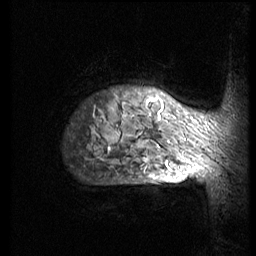
Breast MRI (dynamic contrast-enhanced), one sagittal slice. Position 66 of 74 along the scan axis. 3 images stored at this slice position (order not interpretable as contrast timing). 1.5 T. TE 4.2 ms, TR 8.9 ms. 2.5 mm slice thickness. 256 × 256 image matrix, field of view 200 × 200 mm. Female patient, age 57 years. From the clinical record (not read from this slice): setting: breast cancer imaged before/during neoadjuvant chemotherapy; receptor status: HER2-positive.
Annotated regions visible in this slice (semi-automatically segmented with operator editing):
- analysis volume of interest (the breast-tissue region the enhancement analysis was run in; not a lesion): bounding box [x1, y1, x2, y2] px = [65, 67, 248, 173]
- tumour enhancement mask (voxels above the 140 % enhancement threshold inside the analysis volume of interest): [109, 100, 207, 173]